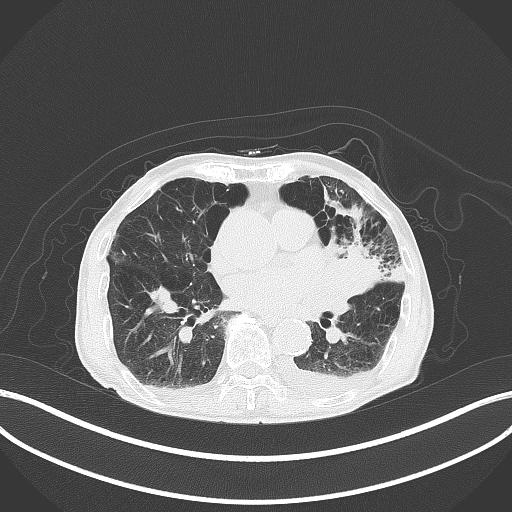
Chest CT, one axial slice. Slice 182 of 227 in the series (ordered by position). Reconstruction kernel B70f. 120 kVp. Lung window (W 1500 / L -600 HU). 3 mm slice thickness. 512 × 512 image matrix, field of view 400 × 400 mm. Patient: male, 90 years or older. Case-level facts recorded for this patient, not image findings: clinical TNM (as recorded): T2b N1 M0.
Outlined on this slice (bounding box drawn by a radiologist):
- lung tumour (recorded histology: squamous cell carcinoma): bounding box <314,231,402,303> (left, top, right, bottom; pixels)